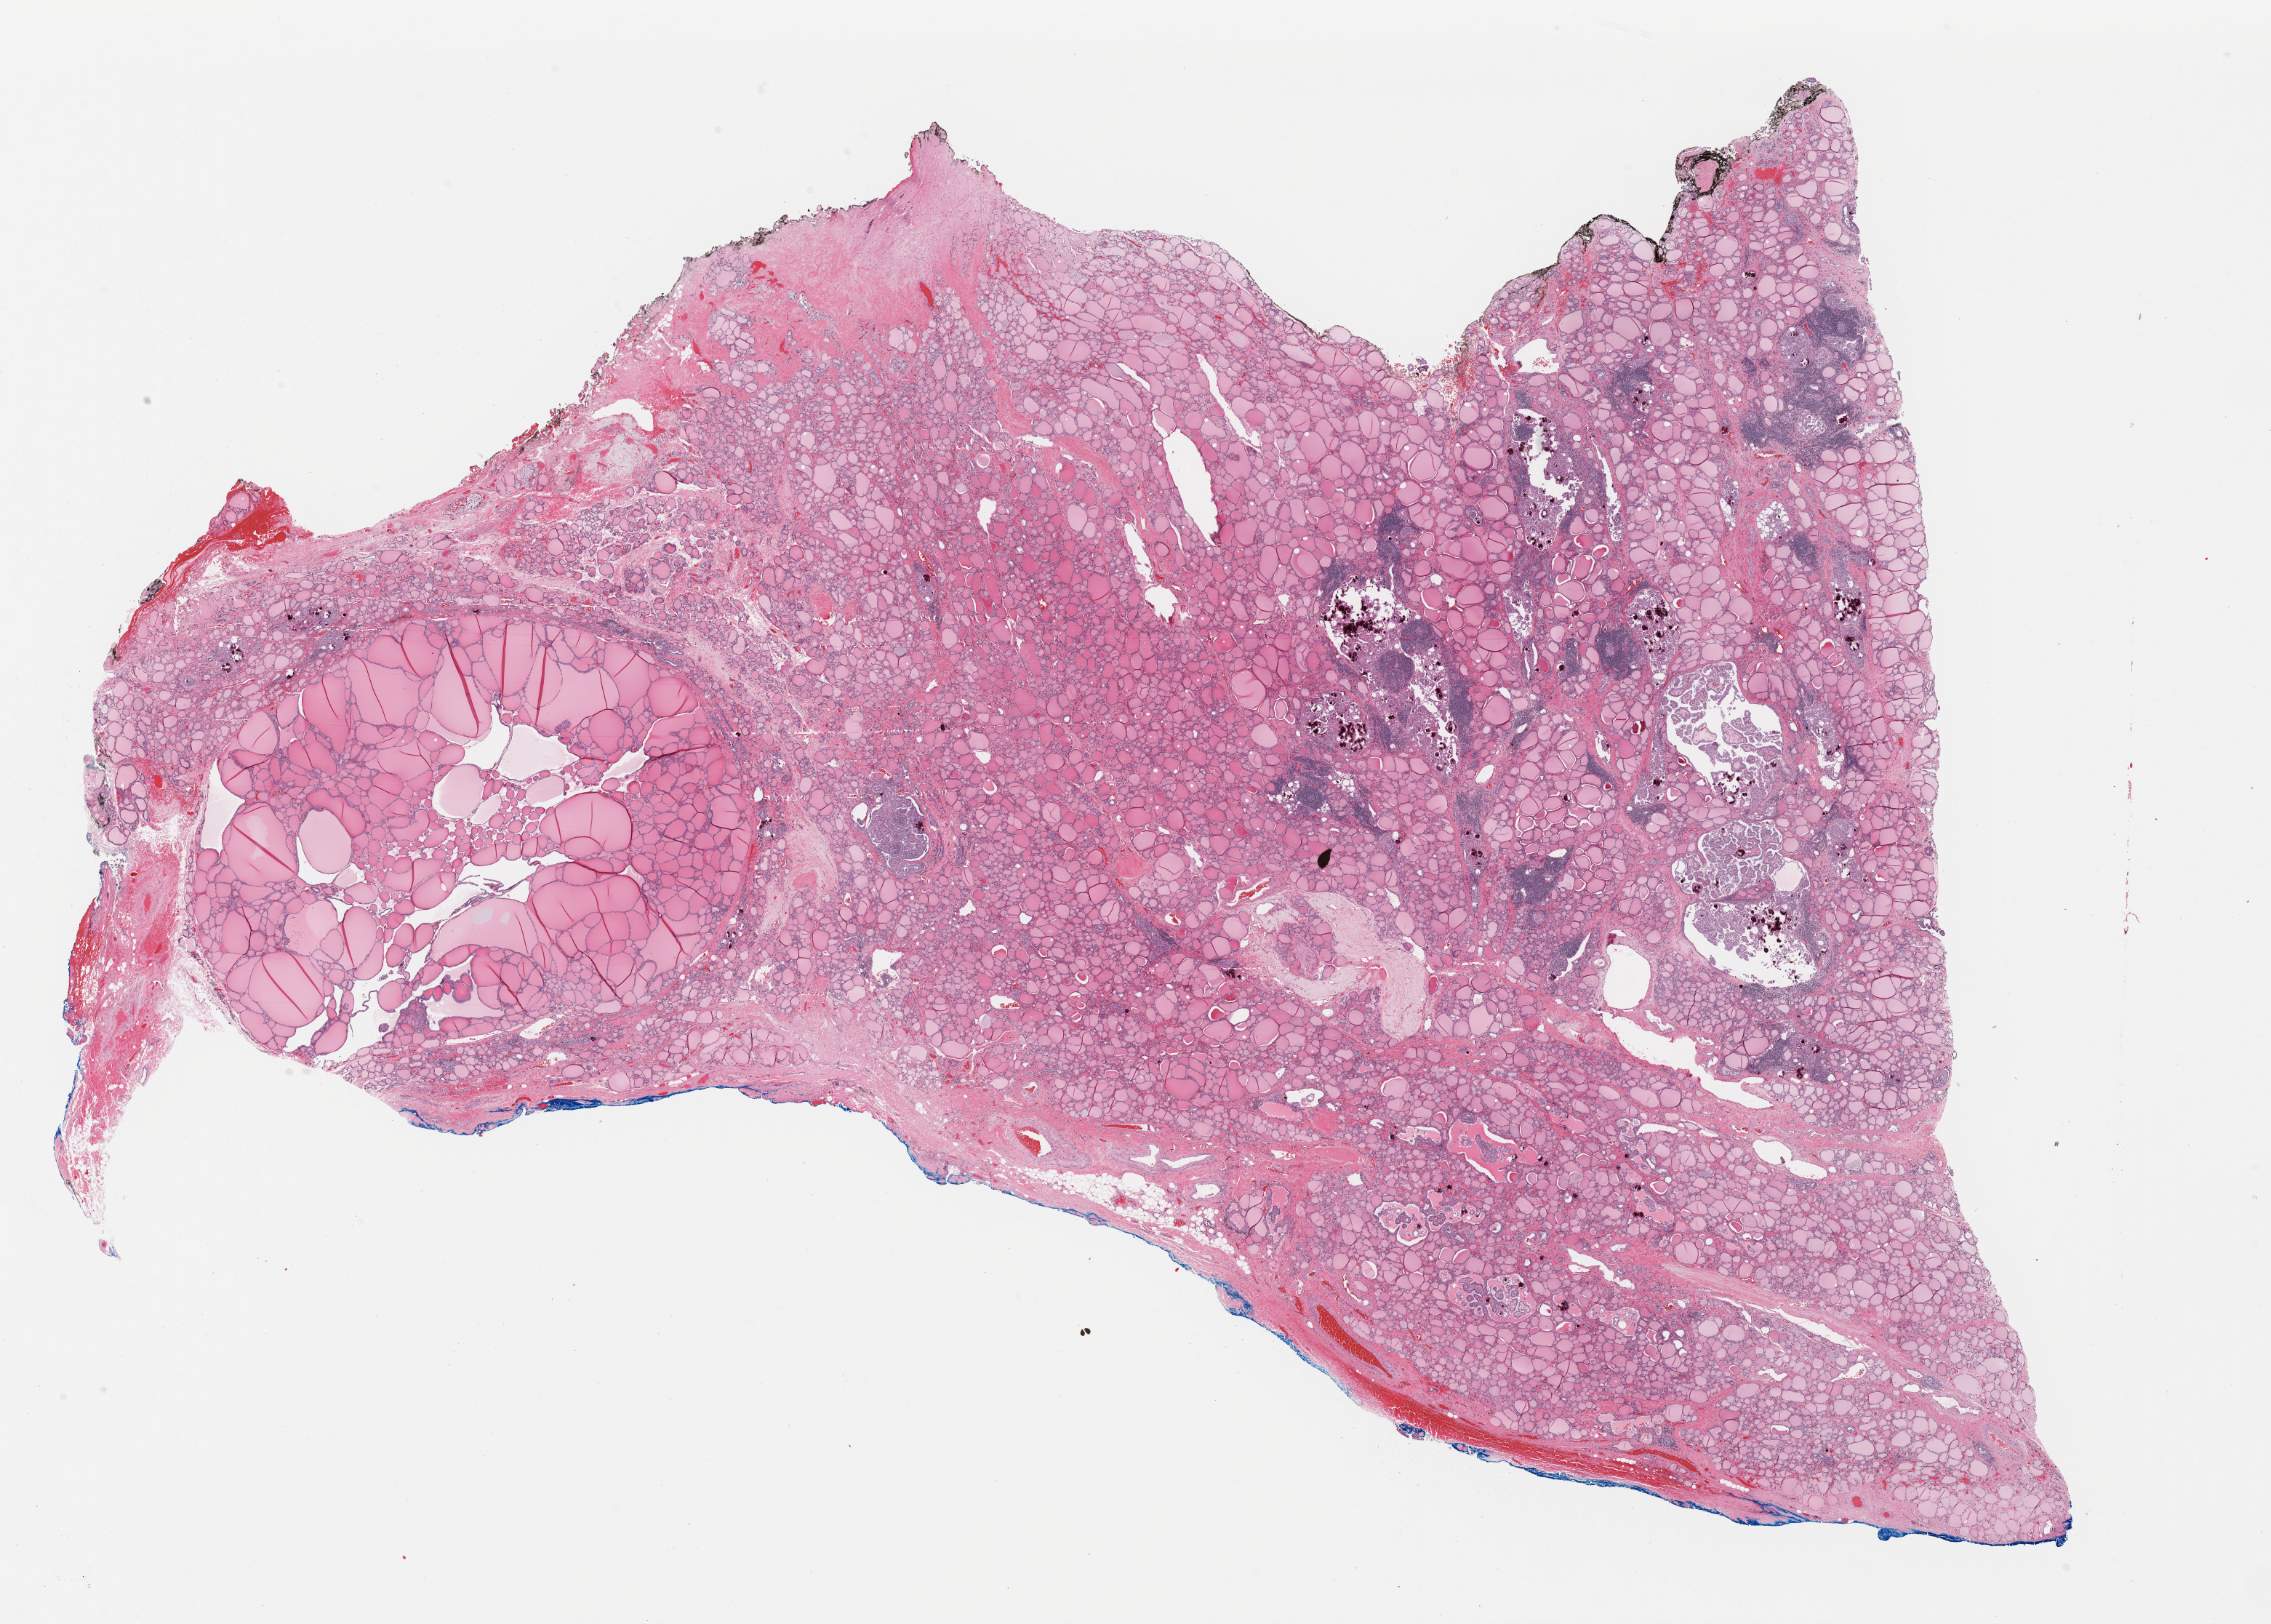
Whole-slide histology image, H&E-stained — a low-resolution overview of the entire scanned area, about 24.6 x 17.6 mm. FFPE section. Sample: primary tumour, thyroid. Patient: male, age at initial diagnosis 60 years.
AJCC pathologic stage: IVA (7th edition). Lymph nodes positive (case pathology): 31 of 99 examined. Diagnosis: Nonencapsulated sclerosing carcinoma (thyroid gland).